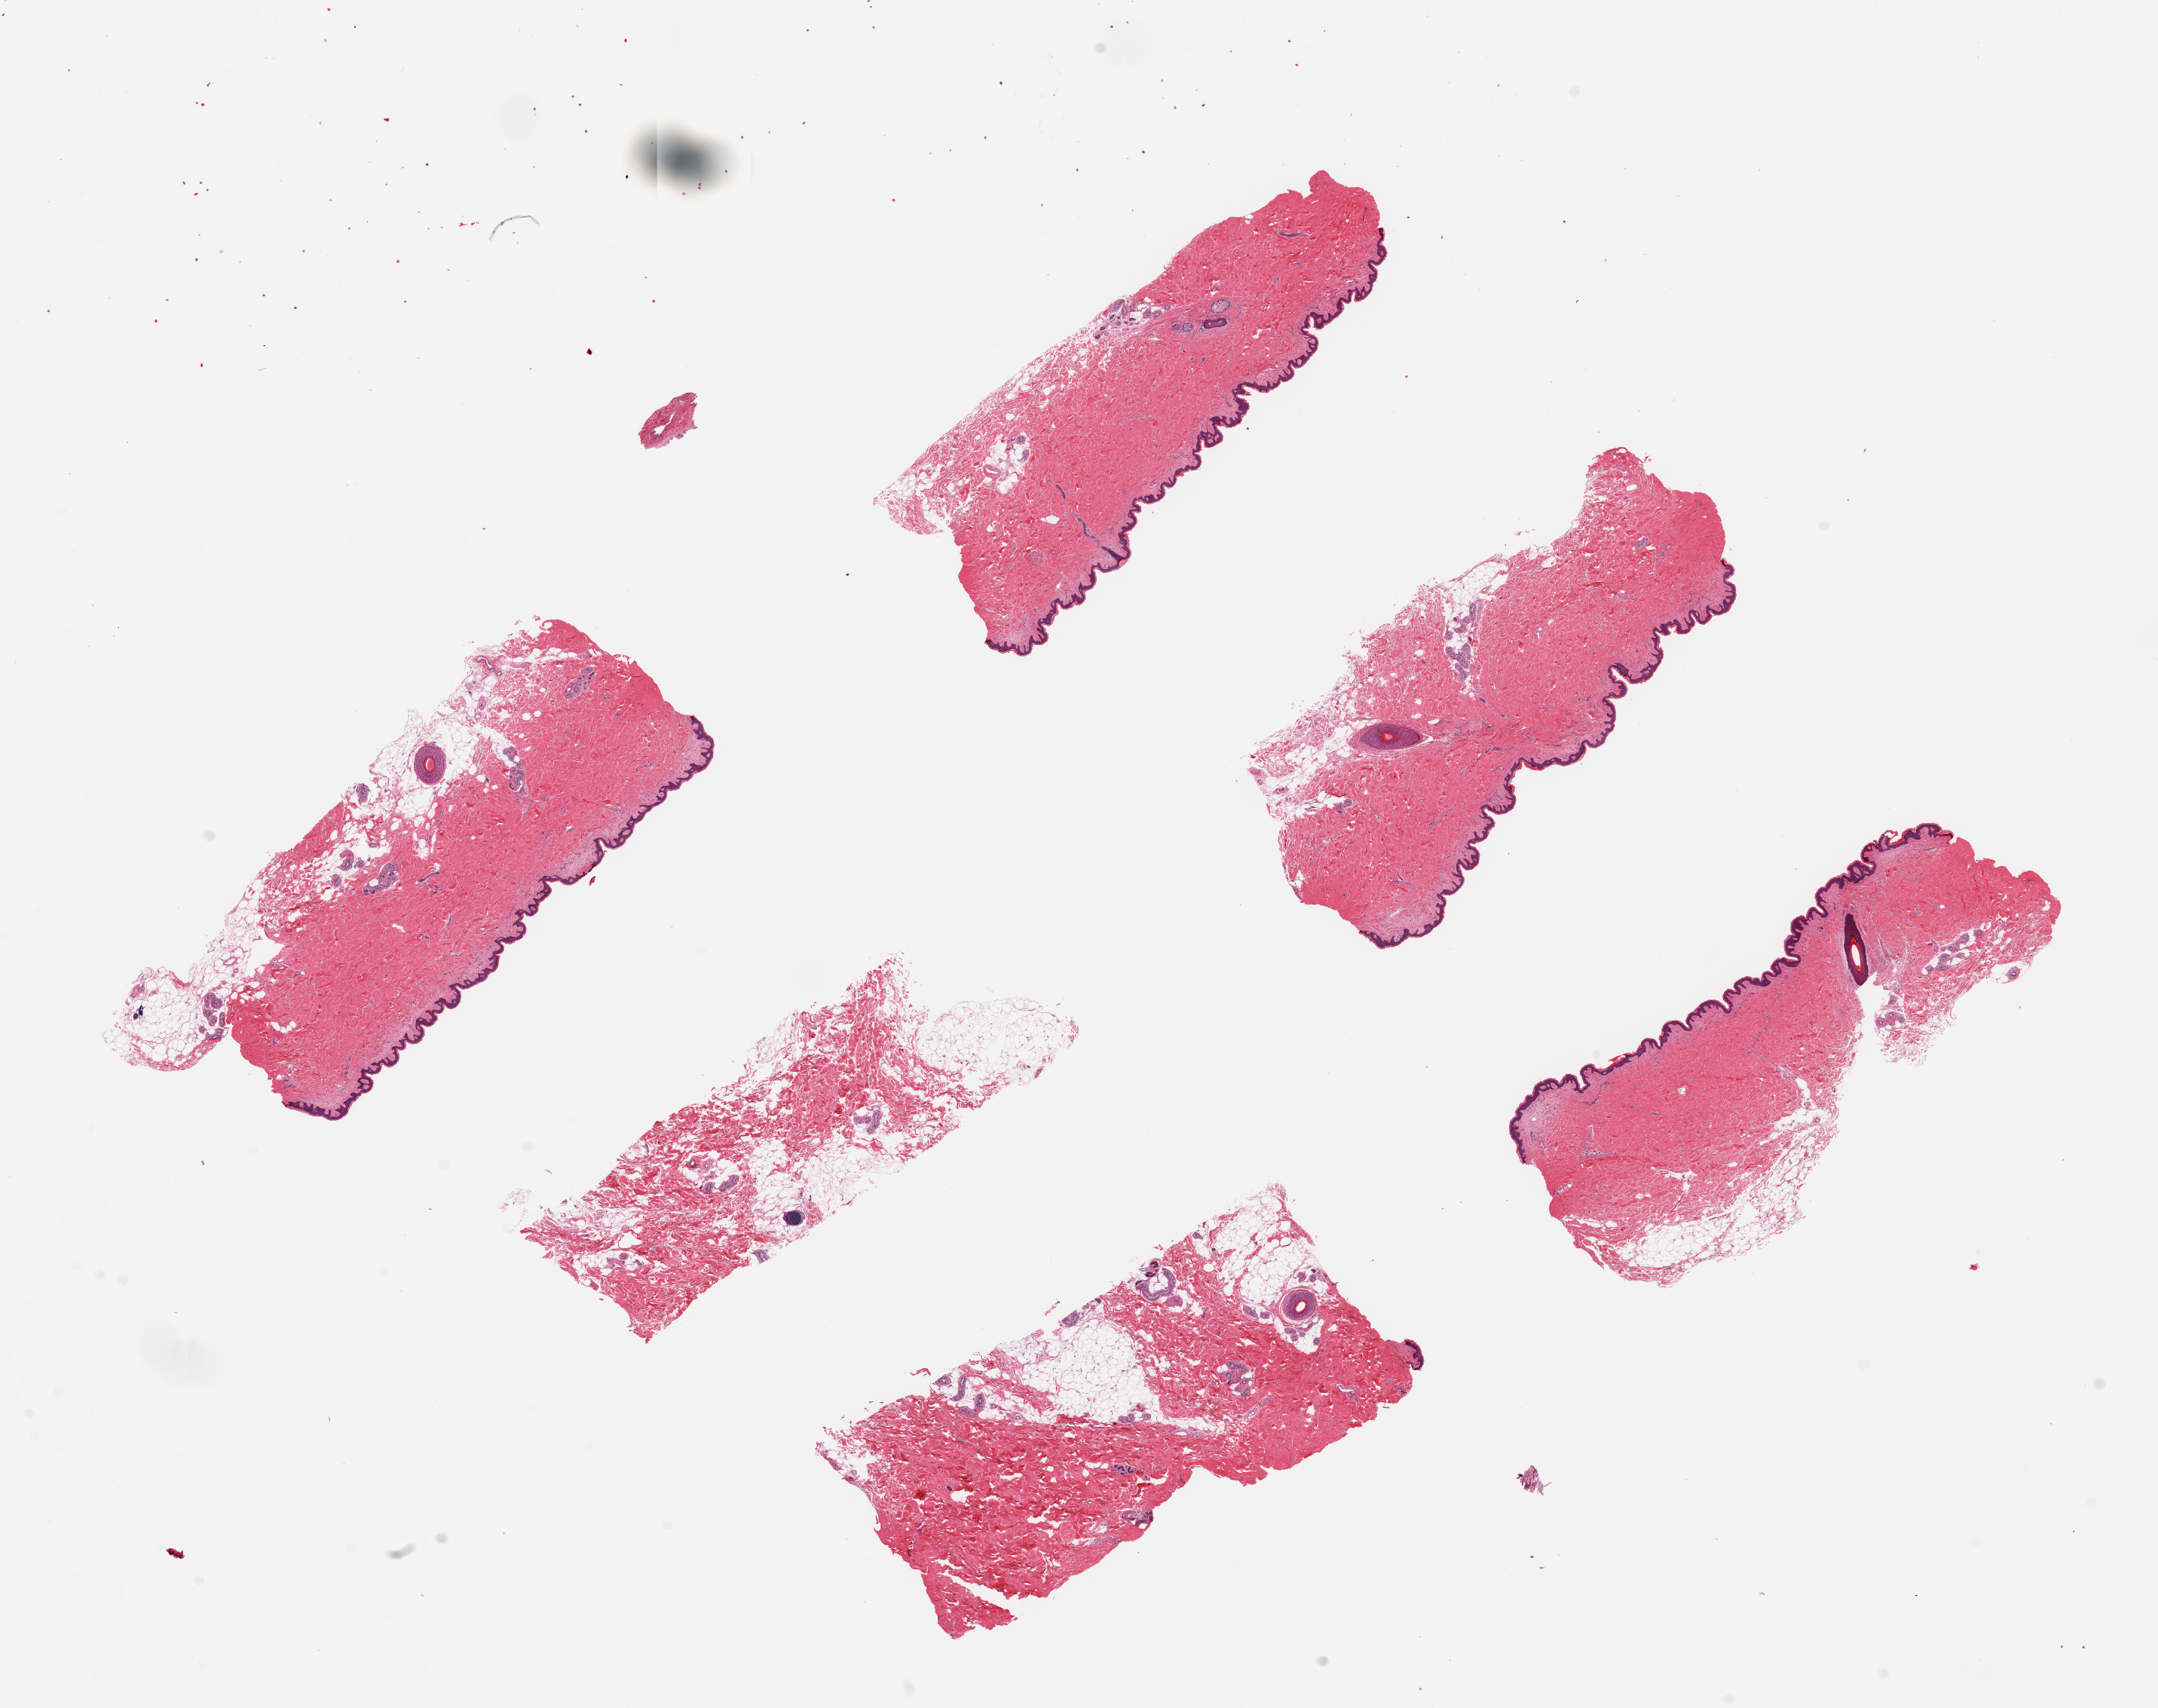
Hematoxylin and eosin (H&E) whole-slide image, shown as a low-resolution overview of the whole scanned area (about 22.6 x 17.9 mm), PAXgene-fixed, paraffin-embedded tissue, target tissue: skin of suprapubic region, tissue donor sample. Donor sex: female.
Reviewer comment on this tissue sample: 6 pieces, up to 6x2.5mm; up to 0.5mm subcutaneous adipose.